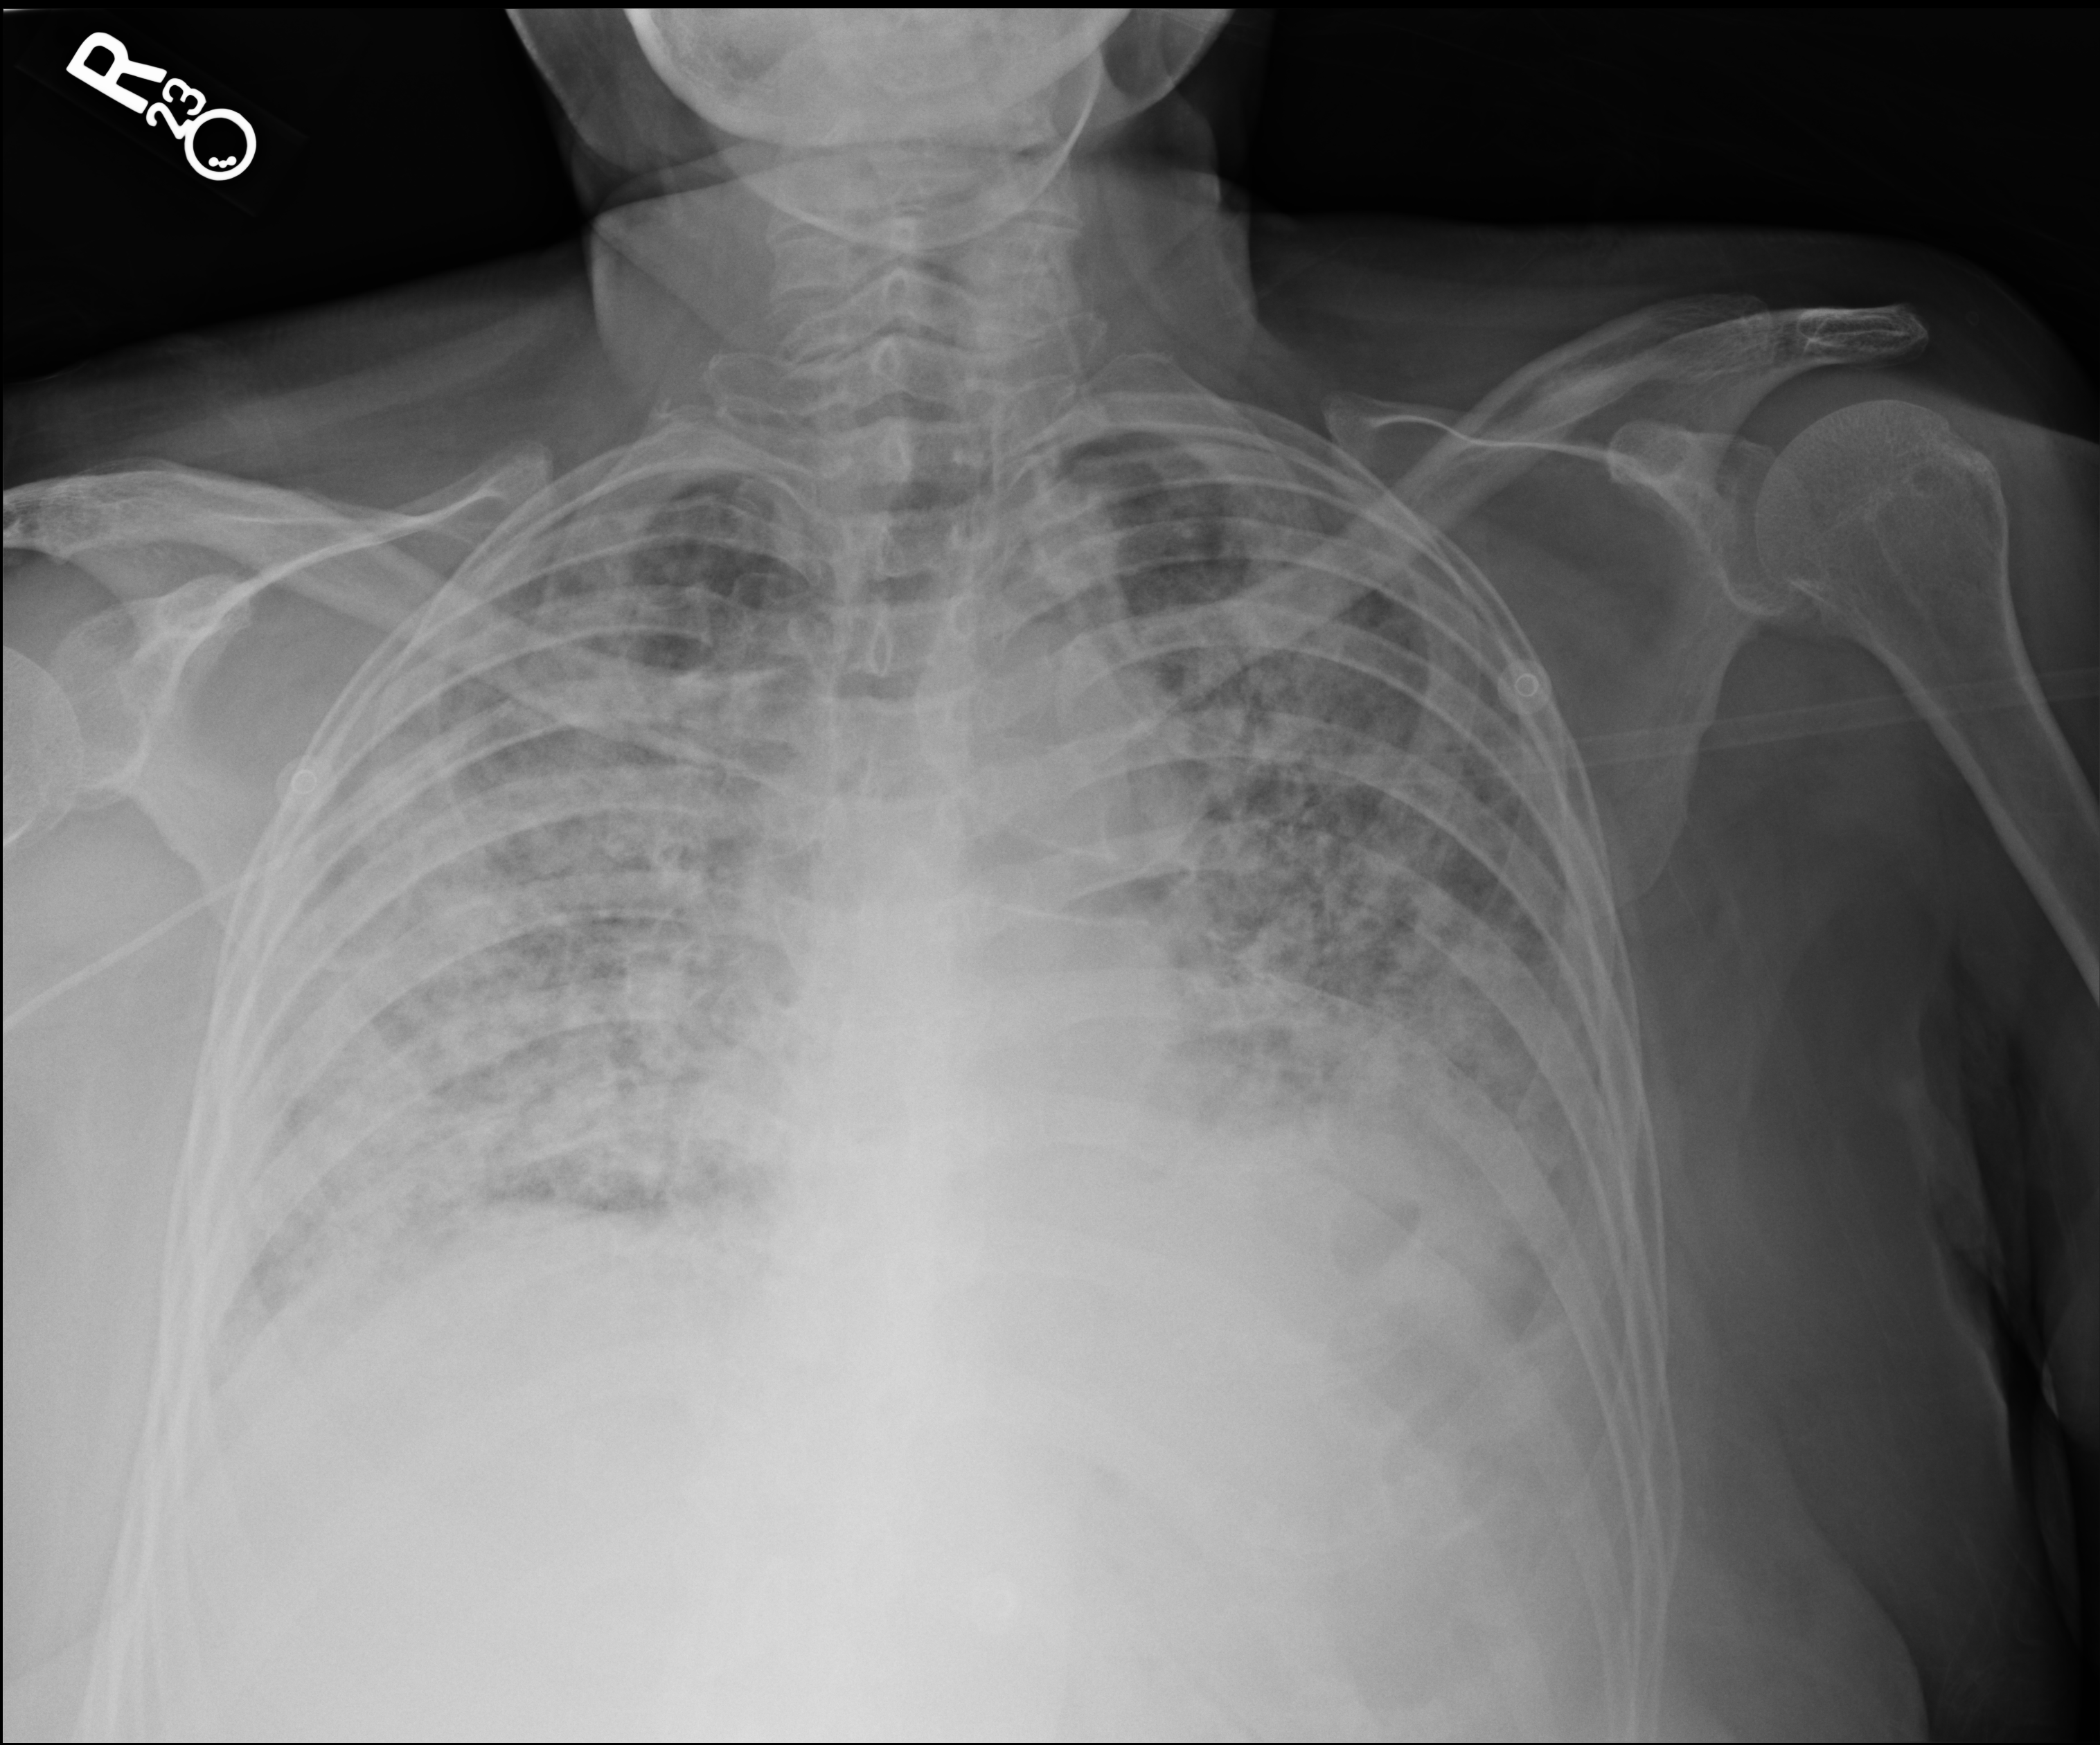
Bedside chest radiograph (computed radiography), anteroposterior (AP) projection. Female patient hospitalised with COVID-19, age 75–90 years.
Admission-level facts for this patient (not findings on this image; timing relative to this image not recorded):
- mechanically ventilated during this hospital stay: yes
- hypertension (admission record): yes